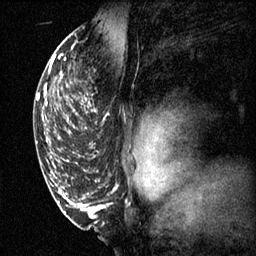
Breast MRI (dynamic contrast-enhanced), one sagittal slice. Slice 40 of 60 in the series (ordered by position). 3 images stored at this slice position (order not interpretable as contrast timing). 1.5 T. TE 4.2 ms, TR 11.1 ms. 2 mm slice thickness. 256 × 256 image matrix, field of view 180 × 180 mm. Female patient, age 50 years.
Outlined on this slice (semi-automatic segmentation, software-assisted and operator-edited):
- analysis volume of interest (the breast-tissue region the enhancement analysis was run in; not a lesion): bounding box <68,68,110,141> (left, top, right, bottom; pixels)
- tumour enhancement mask (voxels above the 70 % enhancement threshold inside the analysis volume of interest): <68,98,93,133>